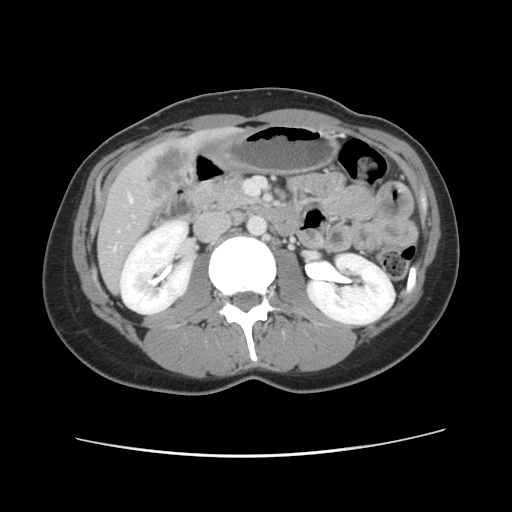
Contrast-enhanced abdominal CT, one axial slice; slice 35 of 134 in the series (ordered by position); intravenous contrast given; soft-tissue window (W 400 / L 40 HU); 512 × 512 image matrix, field of view 339 × 339 mm. Female patient, age 33 years. Case-level facts recorded for this patient, not image findings: diagnosis: colorectal cancer liver metastases, imaged before liver resection; multiple liver metastases: yes.
Annotated regions visible in this slice (outlined manually by an expert reader):
- hepatic veins: bounding box [x1, y1, x2, y2] px = [129, 195, 133, 202]
- liver: [98, 128, 235, 291]
- planned liver remnant (the part of the liver to remain after resection): [99, 242, 124, 291]
- liver metastasis: [148, 147, 196, 202]